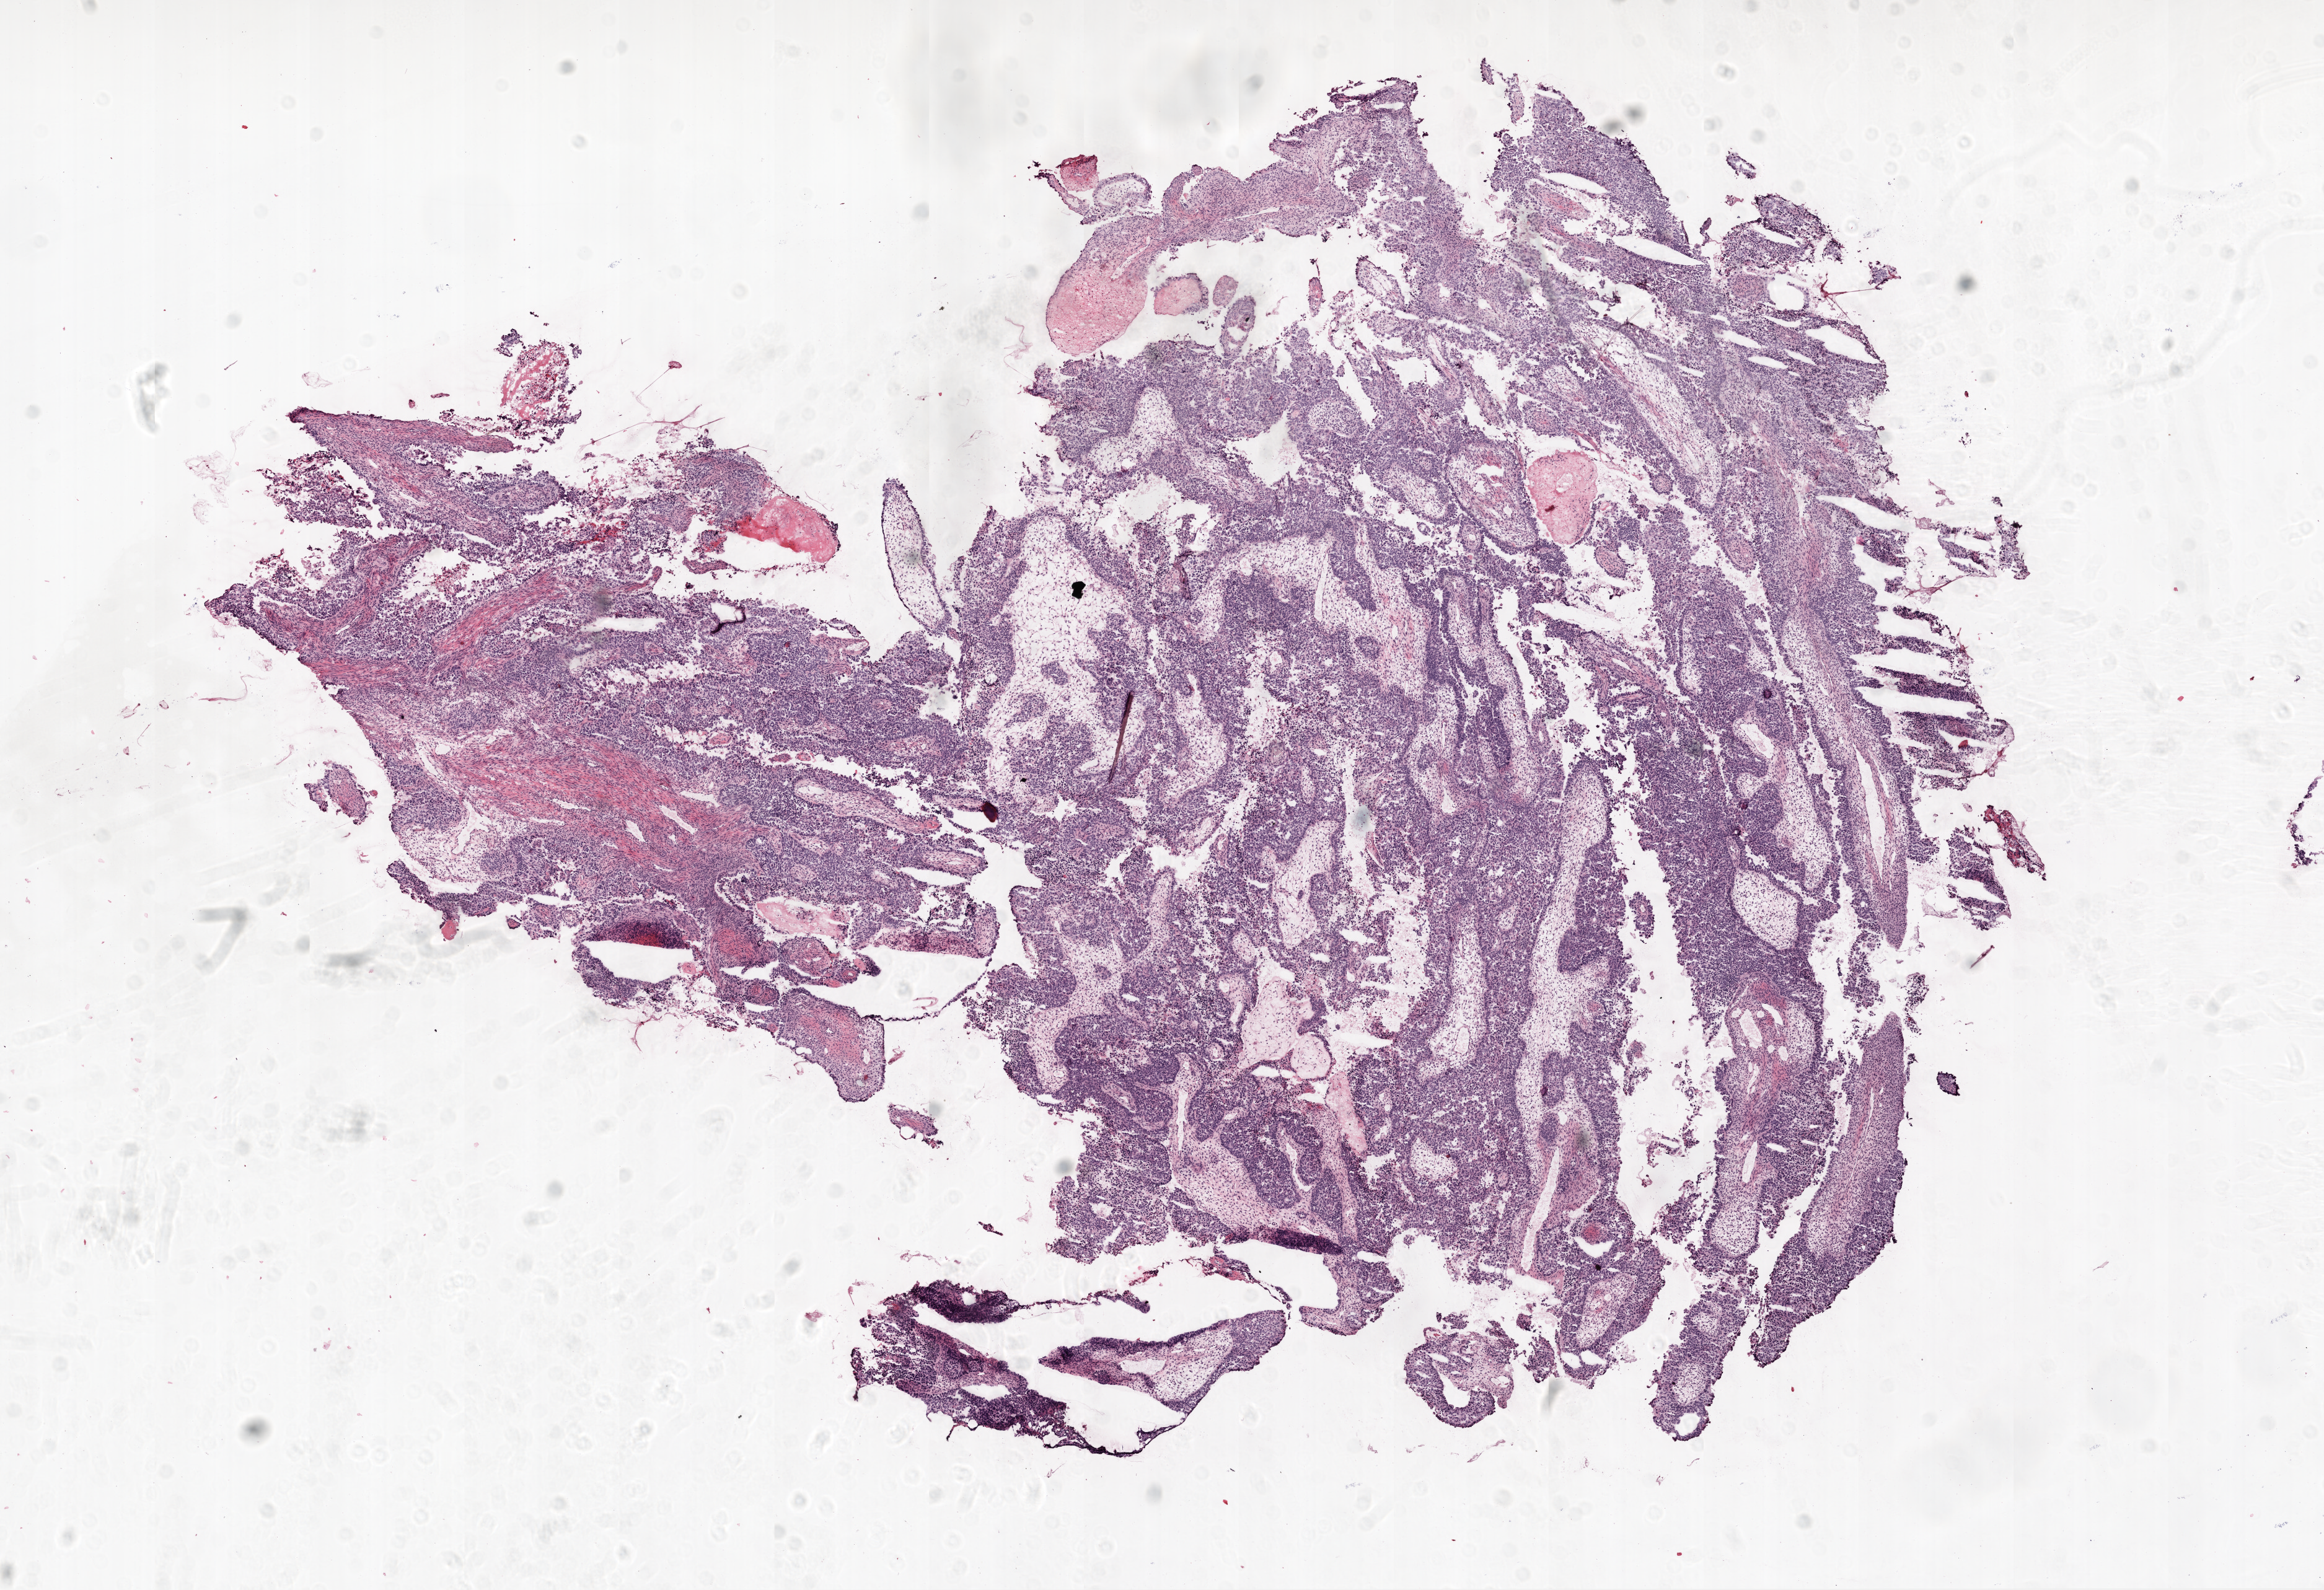
Whole-slide histology image, H&E, whole scanned area (about 15.0 x 10.3 mm, from a 20x scan) shown as a low-resolution overview, frozen section from the top of the tissue portion, ovary, primary tumour sample. Patient: female, age at initial diagnosis 82 years. Histologic grade: G3 (poorly differentiated). Slide review estimates, as recorded: tumour cells 78%, tumour nuclei 90%, normal cells 0%, stromal cells 20%, necrosis 2%.
* FIGO stage: IIIC
* pathologic diagnosis: Serous cystadenocarcinoma, NOS
* laterality: bilateral